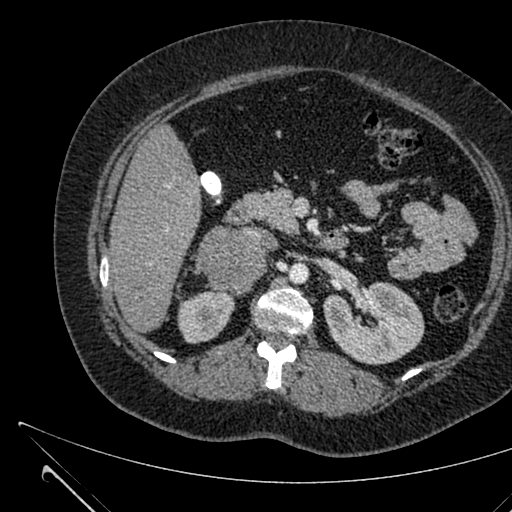
Contrast-enhanced abdominal CT, one axial slice; position 371 of 731 along the scan axis; soft-tissue window (W 400 / L 40 HU); 1 mm slice thickness; 512 × 512 image matrix. Female patient, age 36 years. Case-level facts recorded for this patient, not image findings: diagnosis: adrenocortical carcinoma; tumour side: right adrenal; tumour size at pathology: 10 cm; Ki-67 index: 20 %; stage (as recorded): 4.
Structures marked on this image (semi-automatically segmented with operator editing):
- mass: bounding box (x1, y1, x2, y2) in pixels: (196, 228, 265, 291)